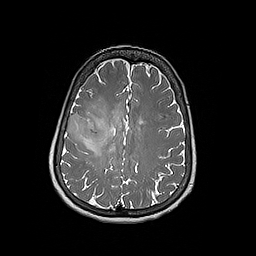
Brain MRI from a brain-tumour surgery series, one axial slice. Slice 73 of 192 in the series (ordered by position). 1 mm slice thickness. 256 × 256 image matrix. Case-level facts recorded for this patient, not image findings: histopathology: Oligodendroglioma; WHO grade: 3; IDH mutation: yes; tumour location: Right Frontal.
Structures marked on this image (outlined manually by an expert reader):
- tumour: bounding box [x1, y1, x2, y2] px = [66, 113, 110, 150]